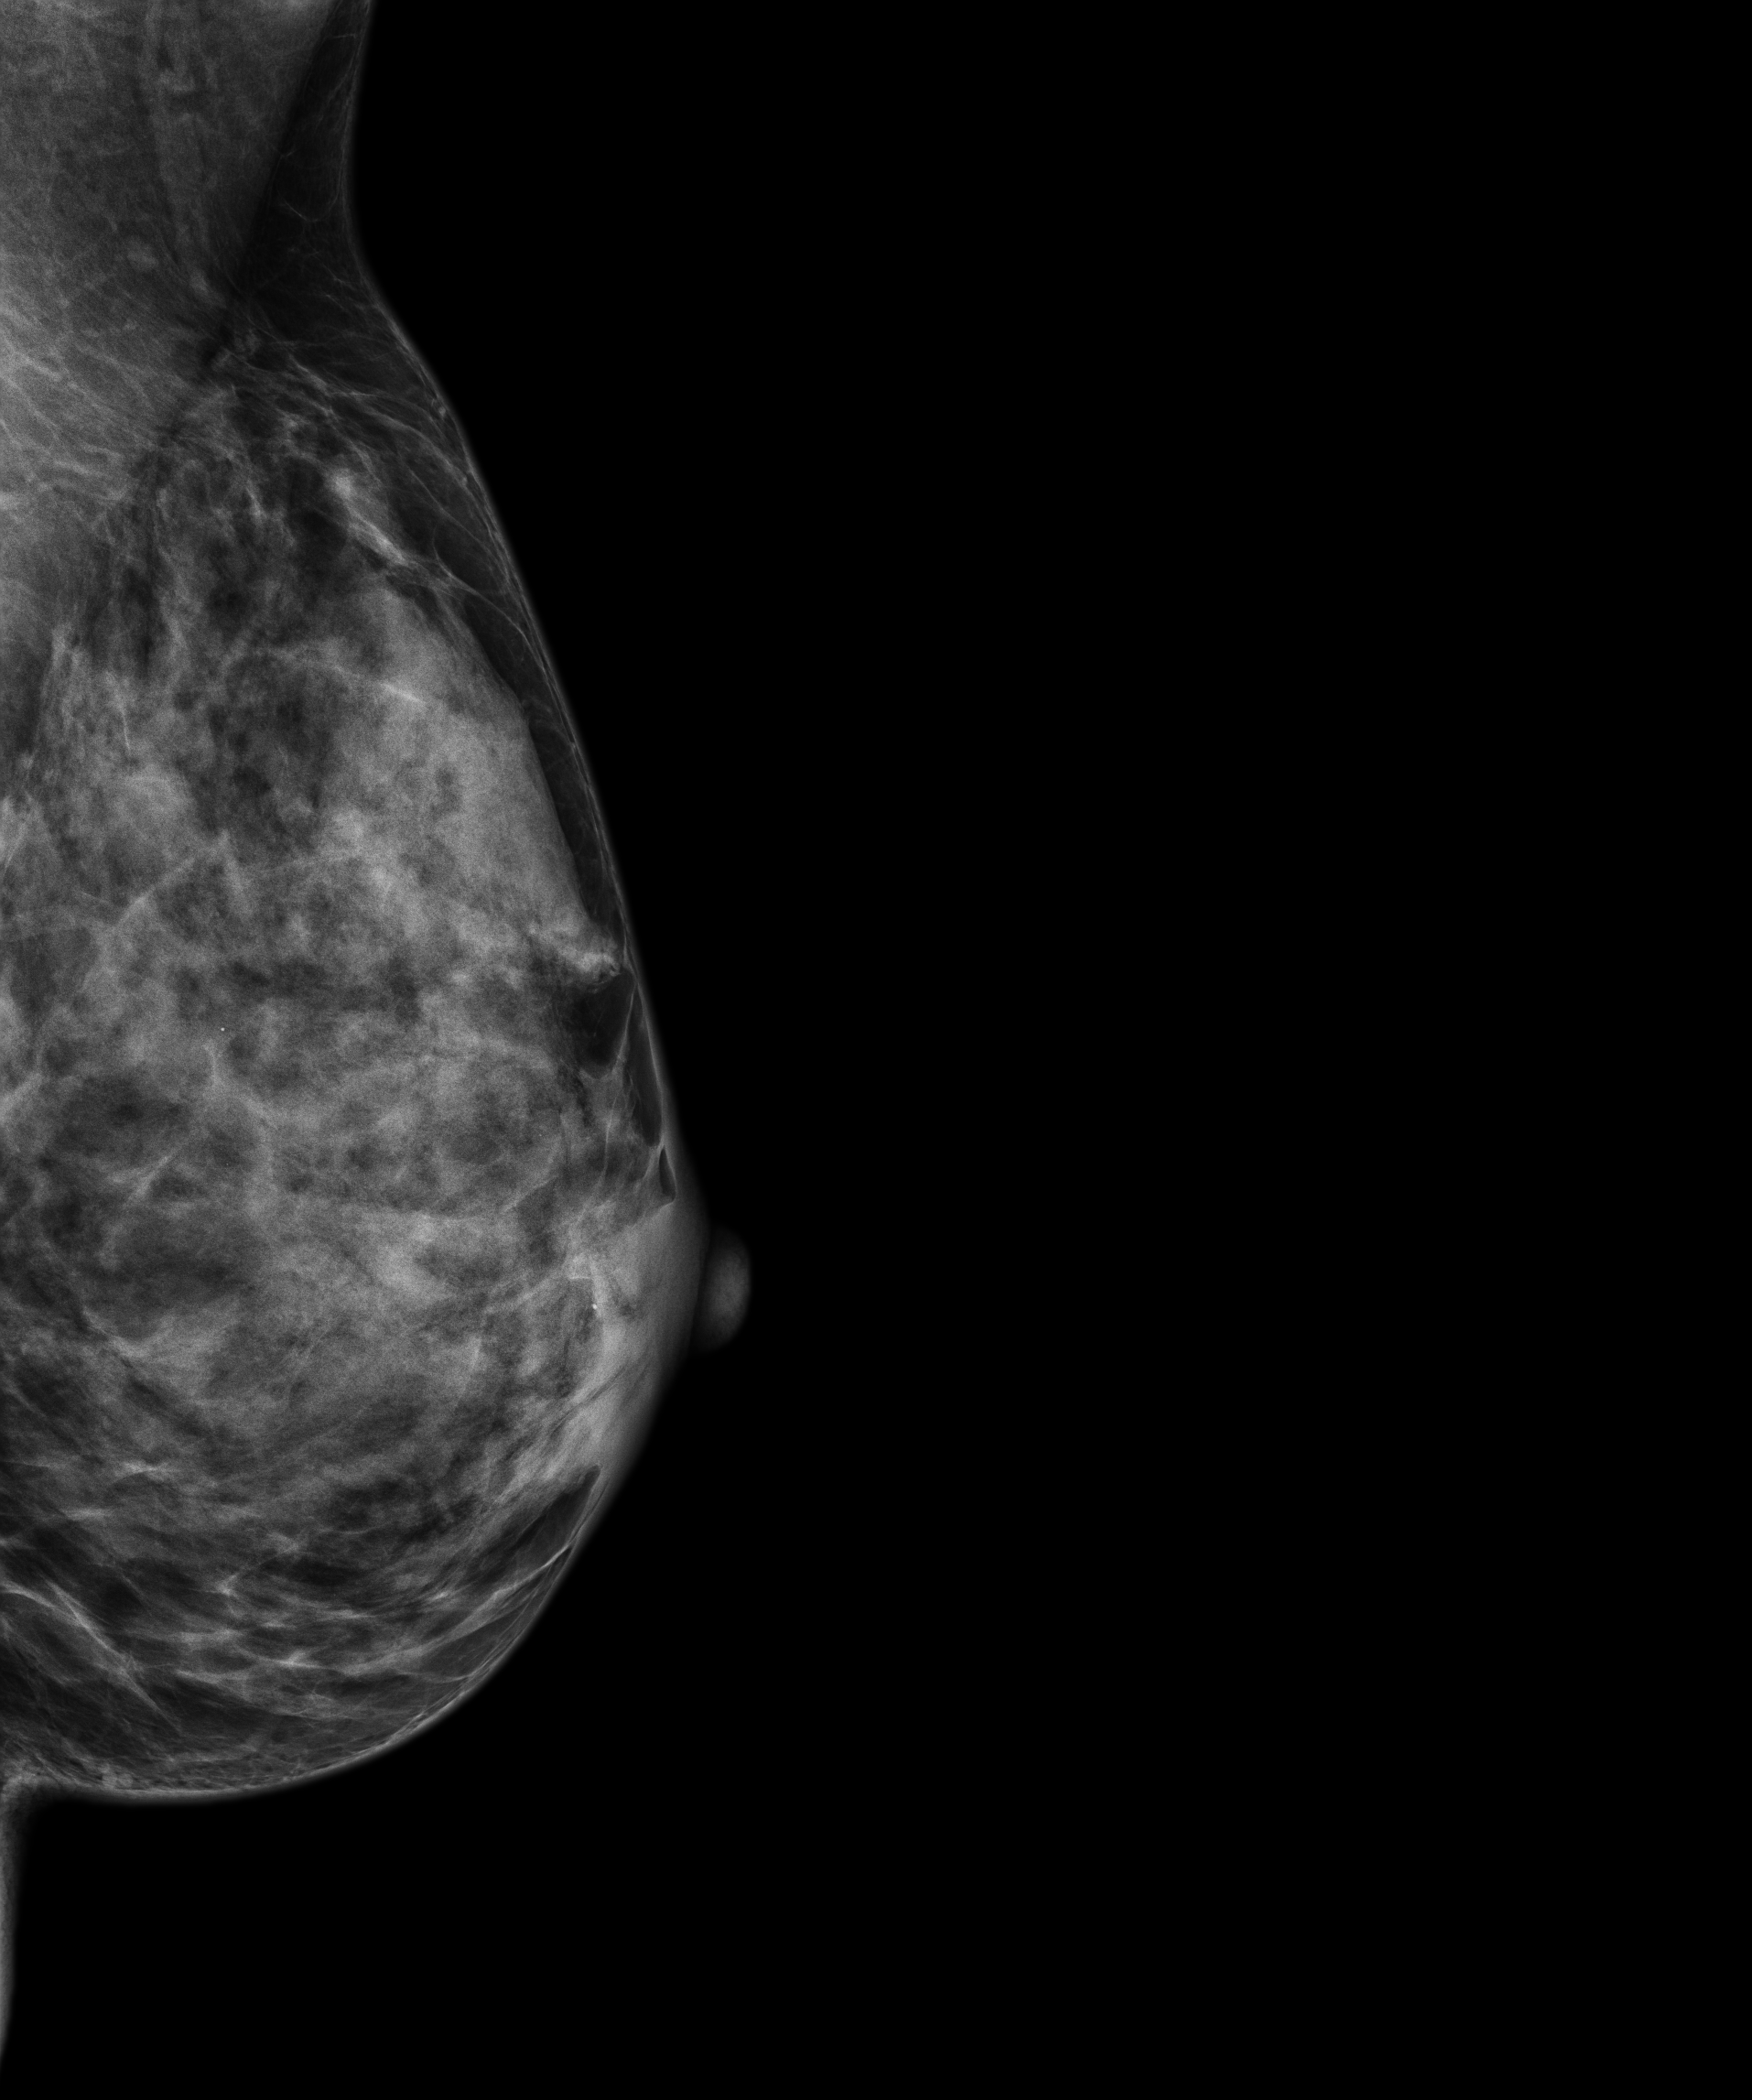
Annual screening mammography examination; compressed breast thickness 34 mm. Female patient, age 45 years.
Image type: full-field digital mammogram. Breast: left. Projection: medio-lateral oblique projection.